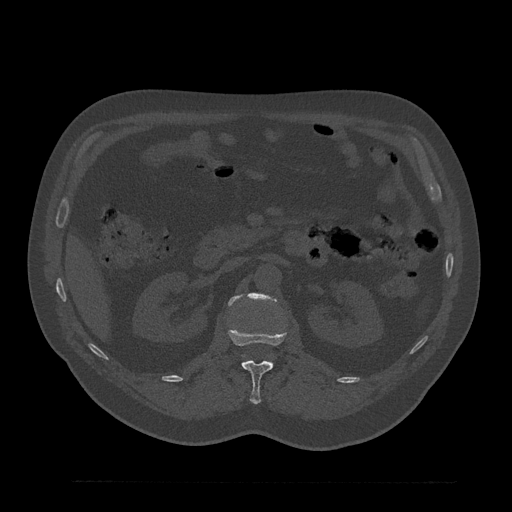
CT including the spine, one axial slice. Bone window (W 1800 / L 400 HU). 512 × 512 image matrix, field of view 430 × 430 mm. Male patient, age 61 years. From the clinical record (not read from this slice): primary cancer: prostate.
Annotated regions visible in this slice (semi-automatic segmentation, software-assisted and operator-edited):
- L1 vertebra: bounding box [x1, y1, x2, y2] px = [228, 325, 287, 405]
- L2 vertebra: [228, 293, 275, 306]